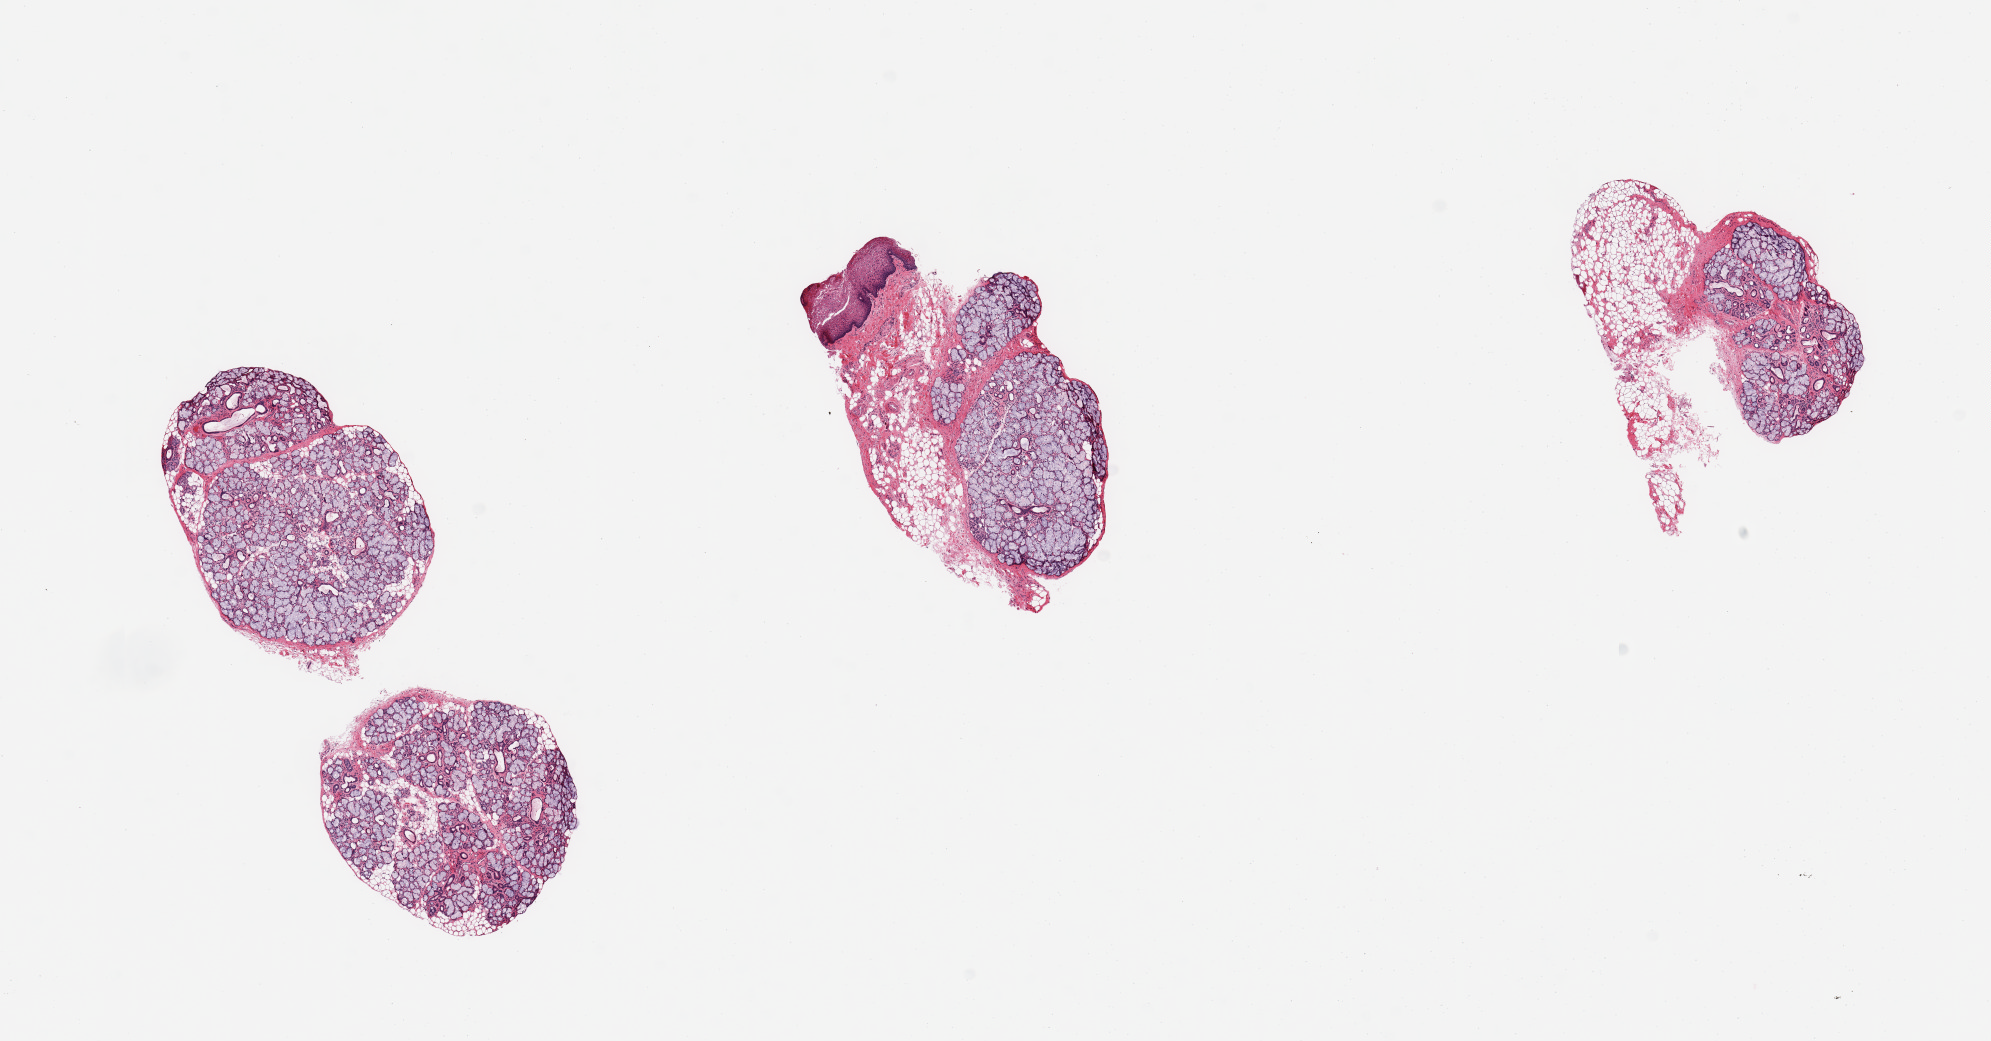
Whole-slide image, H&E stain, whole scanned area (about 15.8 x 8.2 mm, from a 20x scan) shown as a low-resolution overview. Donor sex: male.
Specimen: PAXgene-fixed paraffin-embedded (PFPE) section; section of minor salivary gland (target tissue); tissue donor sample.